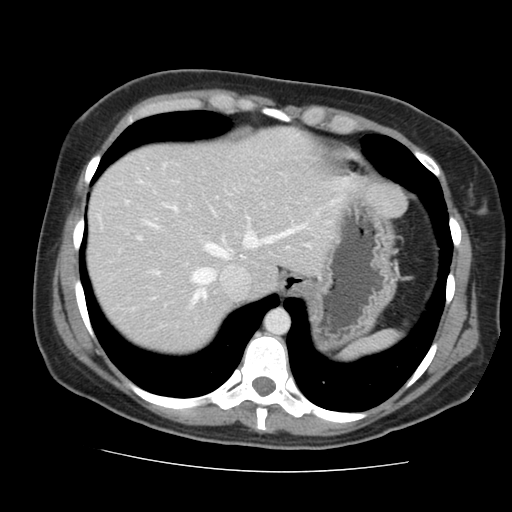
Contrast-enhanced abdominal CT, one axial slice. Position 124 of 144 along the scan axis. Intravenous contrast given. Soft-tissue window (W 400 / L 40 HU). 512 × 512 image matrix. Female patient, age 46 years. From the clinical record (not read from this slice): diagnosis: colorectal cancer liver metastases, imaged before liver resection; multiple liver metastases: no; largest metastasis: 2.8 cm; chemotherapy before resection: yes.
Outlined on this slice (manually delineated by an expert):
- hepatic veins: bounding box (x1, y1, x2, y2) in pixels: (147, 194, 345, 304)
- liver: (88, 129, 341, 355)
- planned liver remnant (the part of the liver to remain after resection): (88, 129, 340, 355)
- portal vein (with intrahepatic branches): (138, 238, 158, 274)